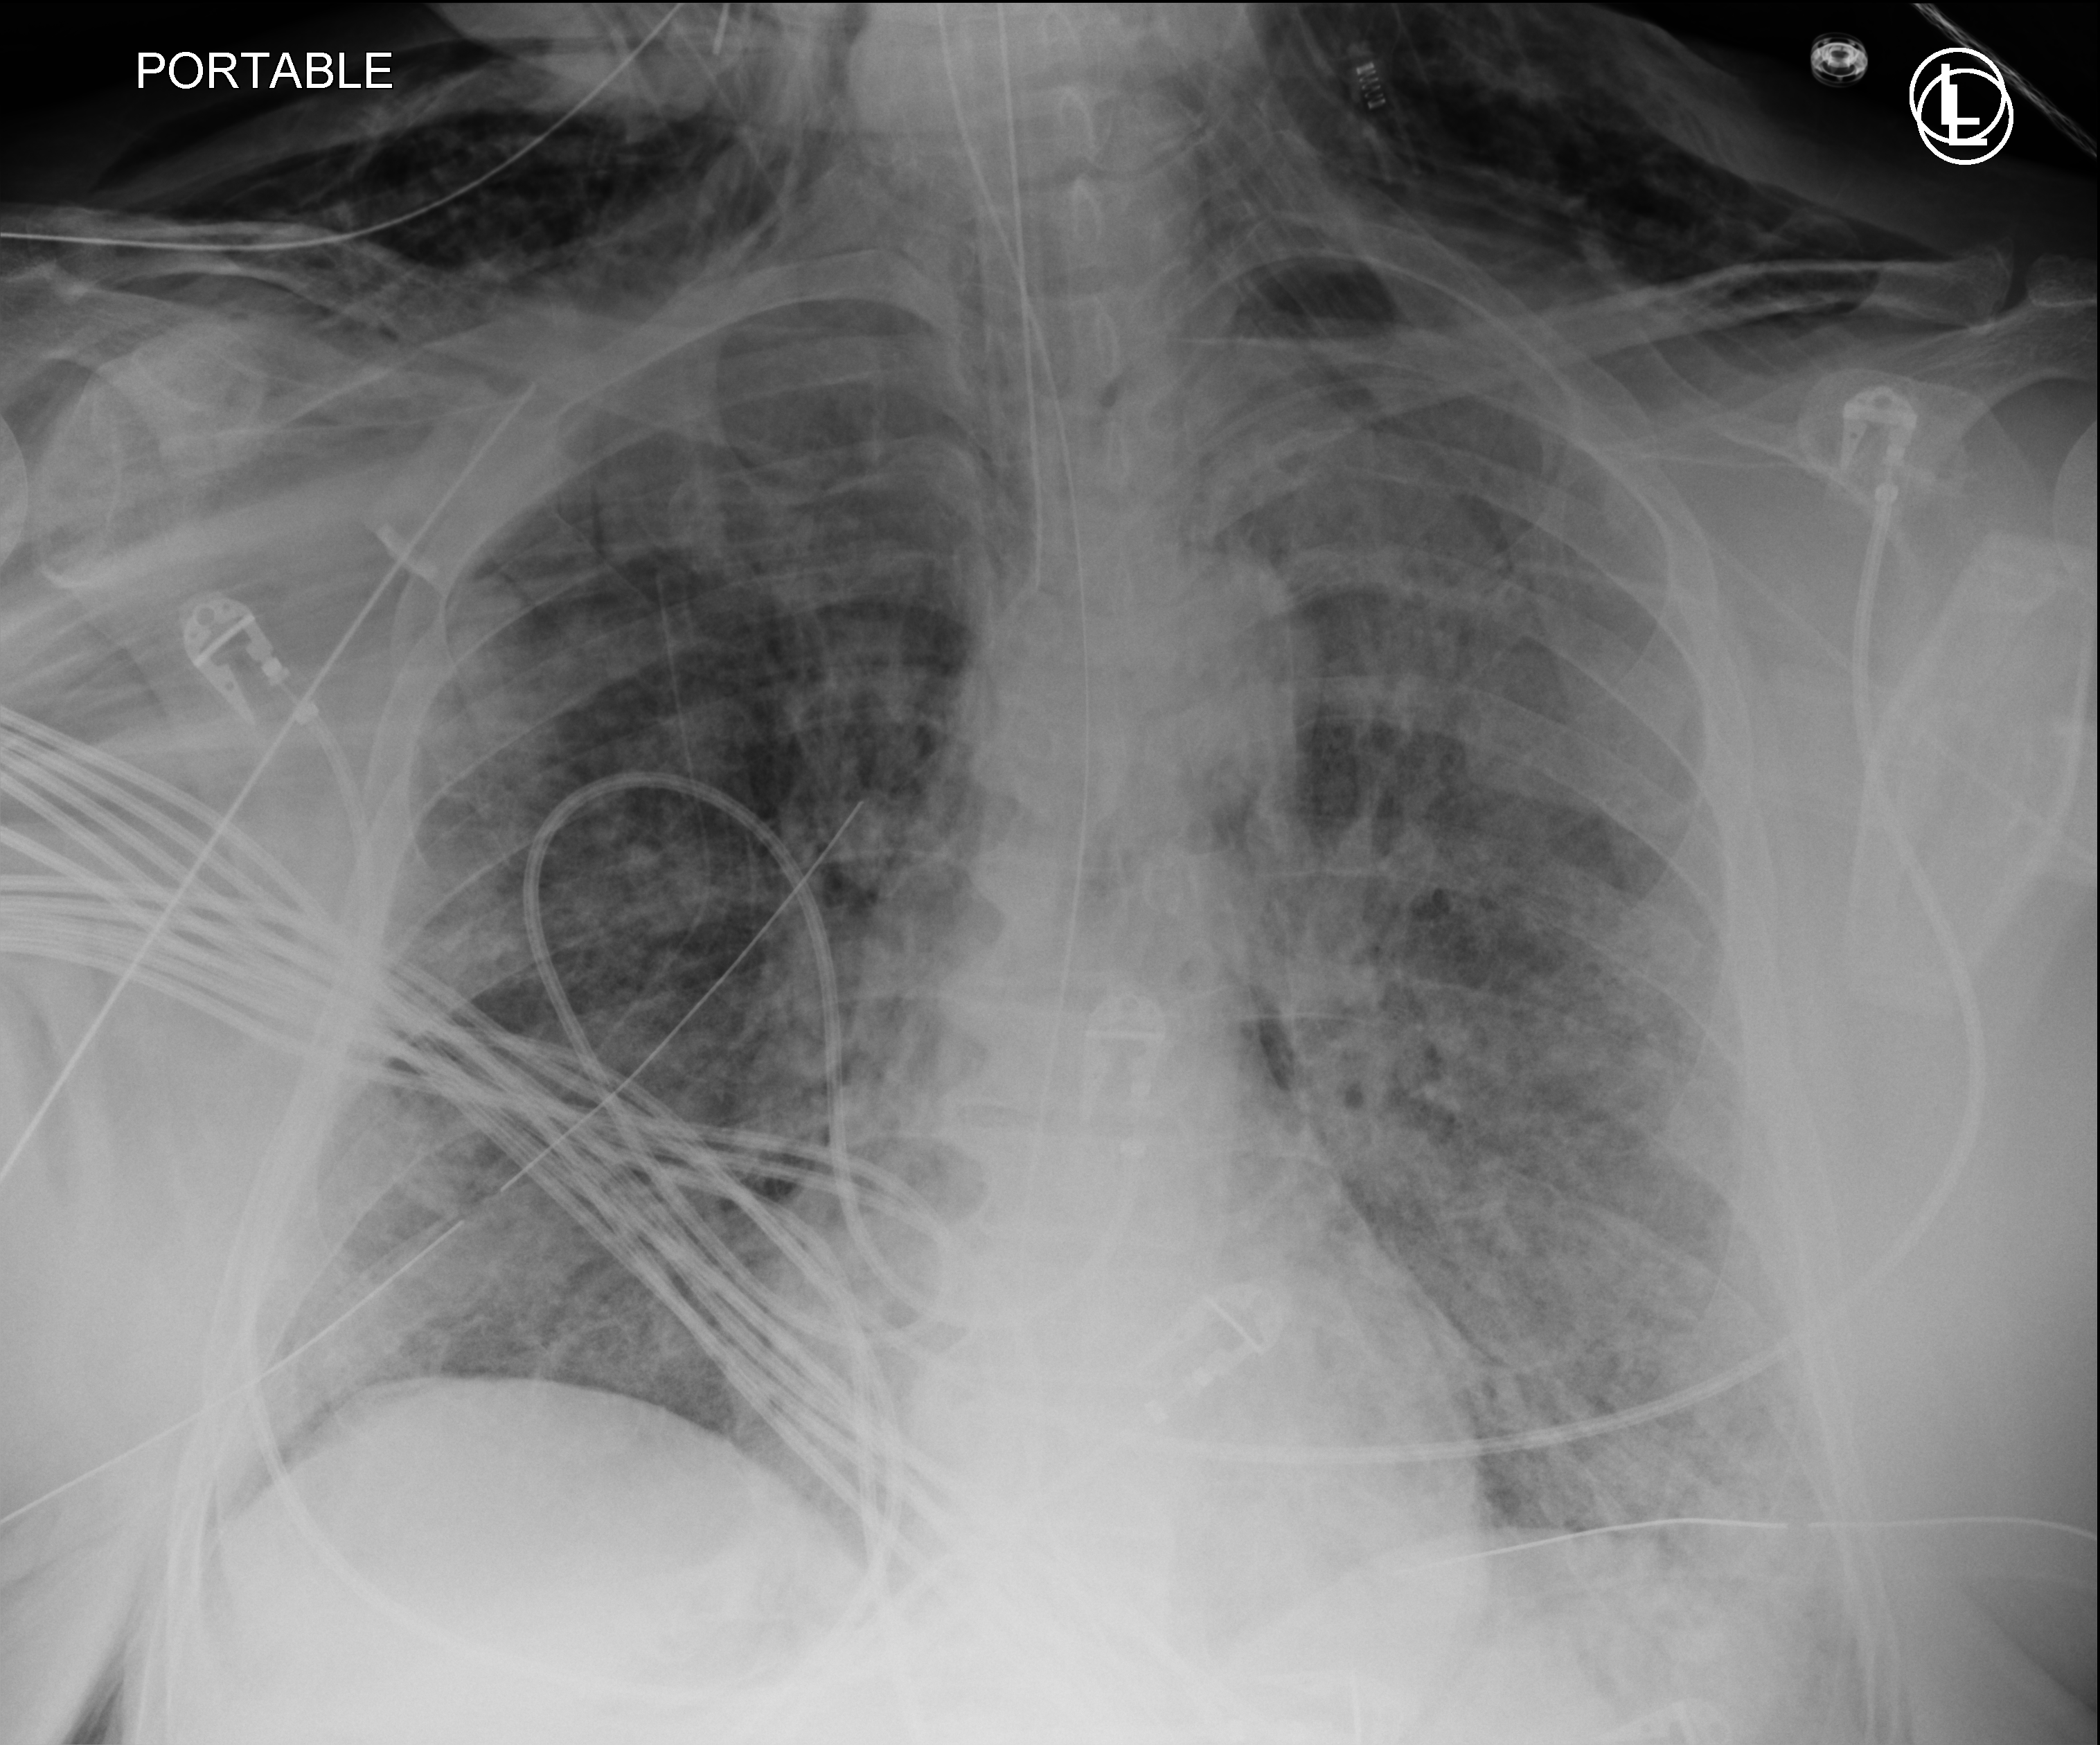
Portable chest radiograph; anteroposterior (AP) projection. Patient hospitalised with COVID-19, aged 18–59 years.
Hospital-stay facts (about this admission, not read from this image; timing relative to this image not recorded): smoking status (admission record): never; admitted to intensive care during this hospital stay: yes; length of hospital stay: 28 days.